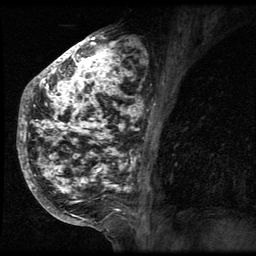
Breast MRI (dynamic contrast-enhanced), one sagittal slice; 3 images stored at this slice position (order not interpretable as contrast timing); 1.5 T; TE 4.2 ms, TR 9 ms; 2.5 mm slice thickness; 256 × 256 image matrix, field of view 180 × 180 mm. Female patient, age 50 years. Case-level facts recorded for this patient, not image findings: setting: breast cancer imaged before/during neoadjuvant chemotherapy; receptor status: triple-negative.
Annotated regions visible in this slice (semi-automatic segmentation, software-assisted and operator-edited):
- analysis volume of interest (the breast-tissue region the enhancement analysis was run in; not a lesion): bounding box [x1, y1, x2, y2] px = [24, 39, 142, 212]
- tumour enhancement mask (voxels above the 140 % enhancement threshold inside the analysis volume of interest): [24, 39, 142, 212]